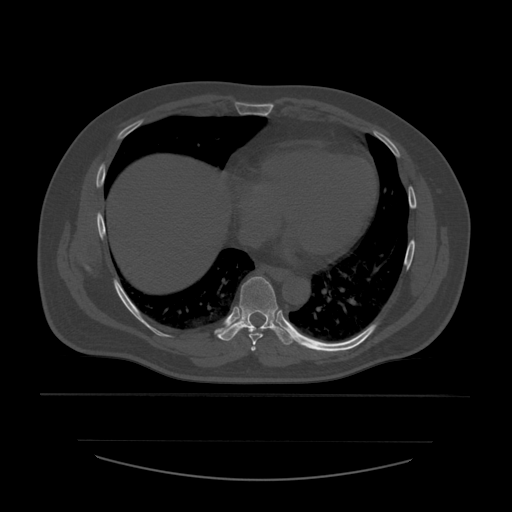
CT including the spine, one axial slice. Slice 345 of 532 in the series (ordered by position). Reconstruction kernel STANDARD. Bone window (W 1800 / L 400 HU). 512 × 512 image matrix. Patient age 44 years. Case-level facts recorded for this patient, not image findings: primary cancer: soft tissue sarcoma.
Outlined on this slice (semi-automatic segmentation, software-assisted and operator-edited):
- T6 vertebra: bounding box [x1, y1, x2, y2] px = [251, 346, 256, 353]
- T7 vertebra: [249, 333, 264, 346]
- T8 vertebra: [217, 277, 297, 345]